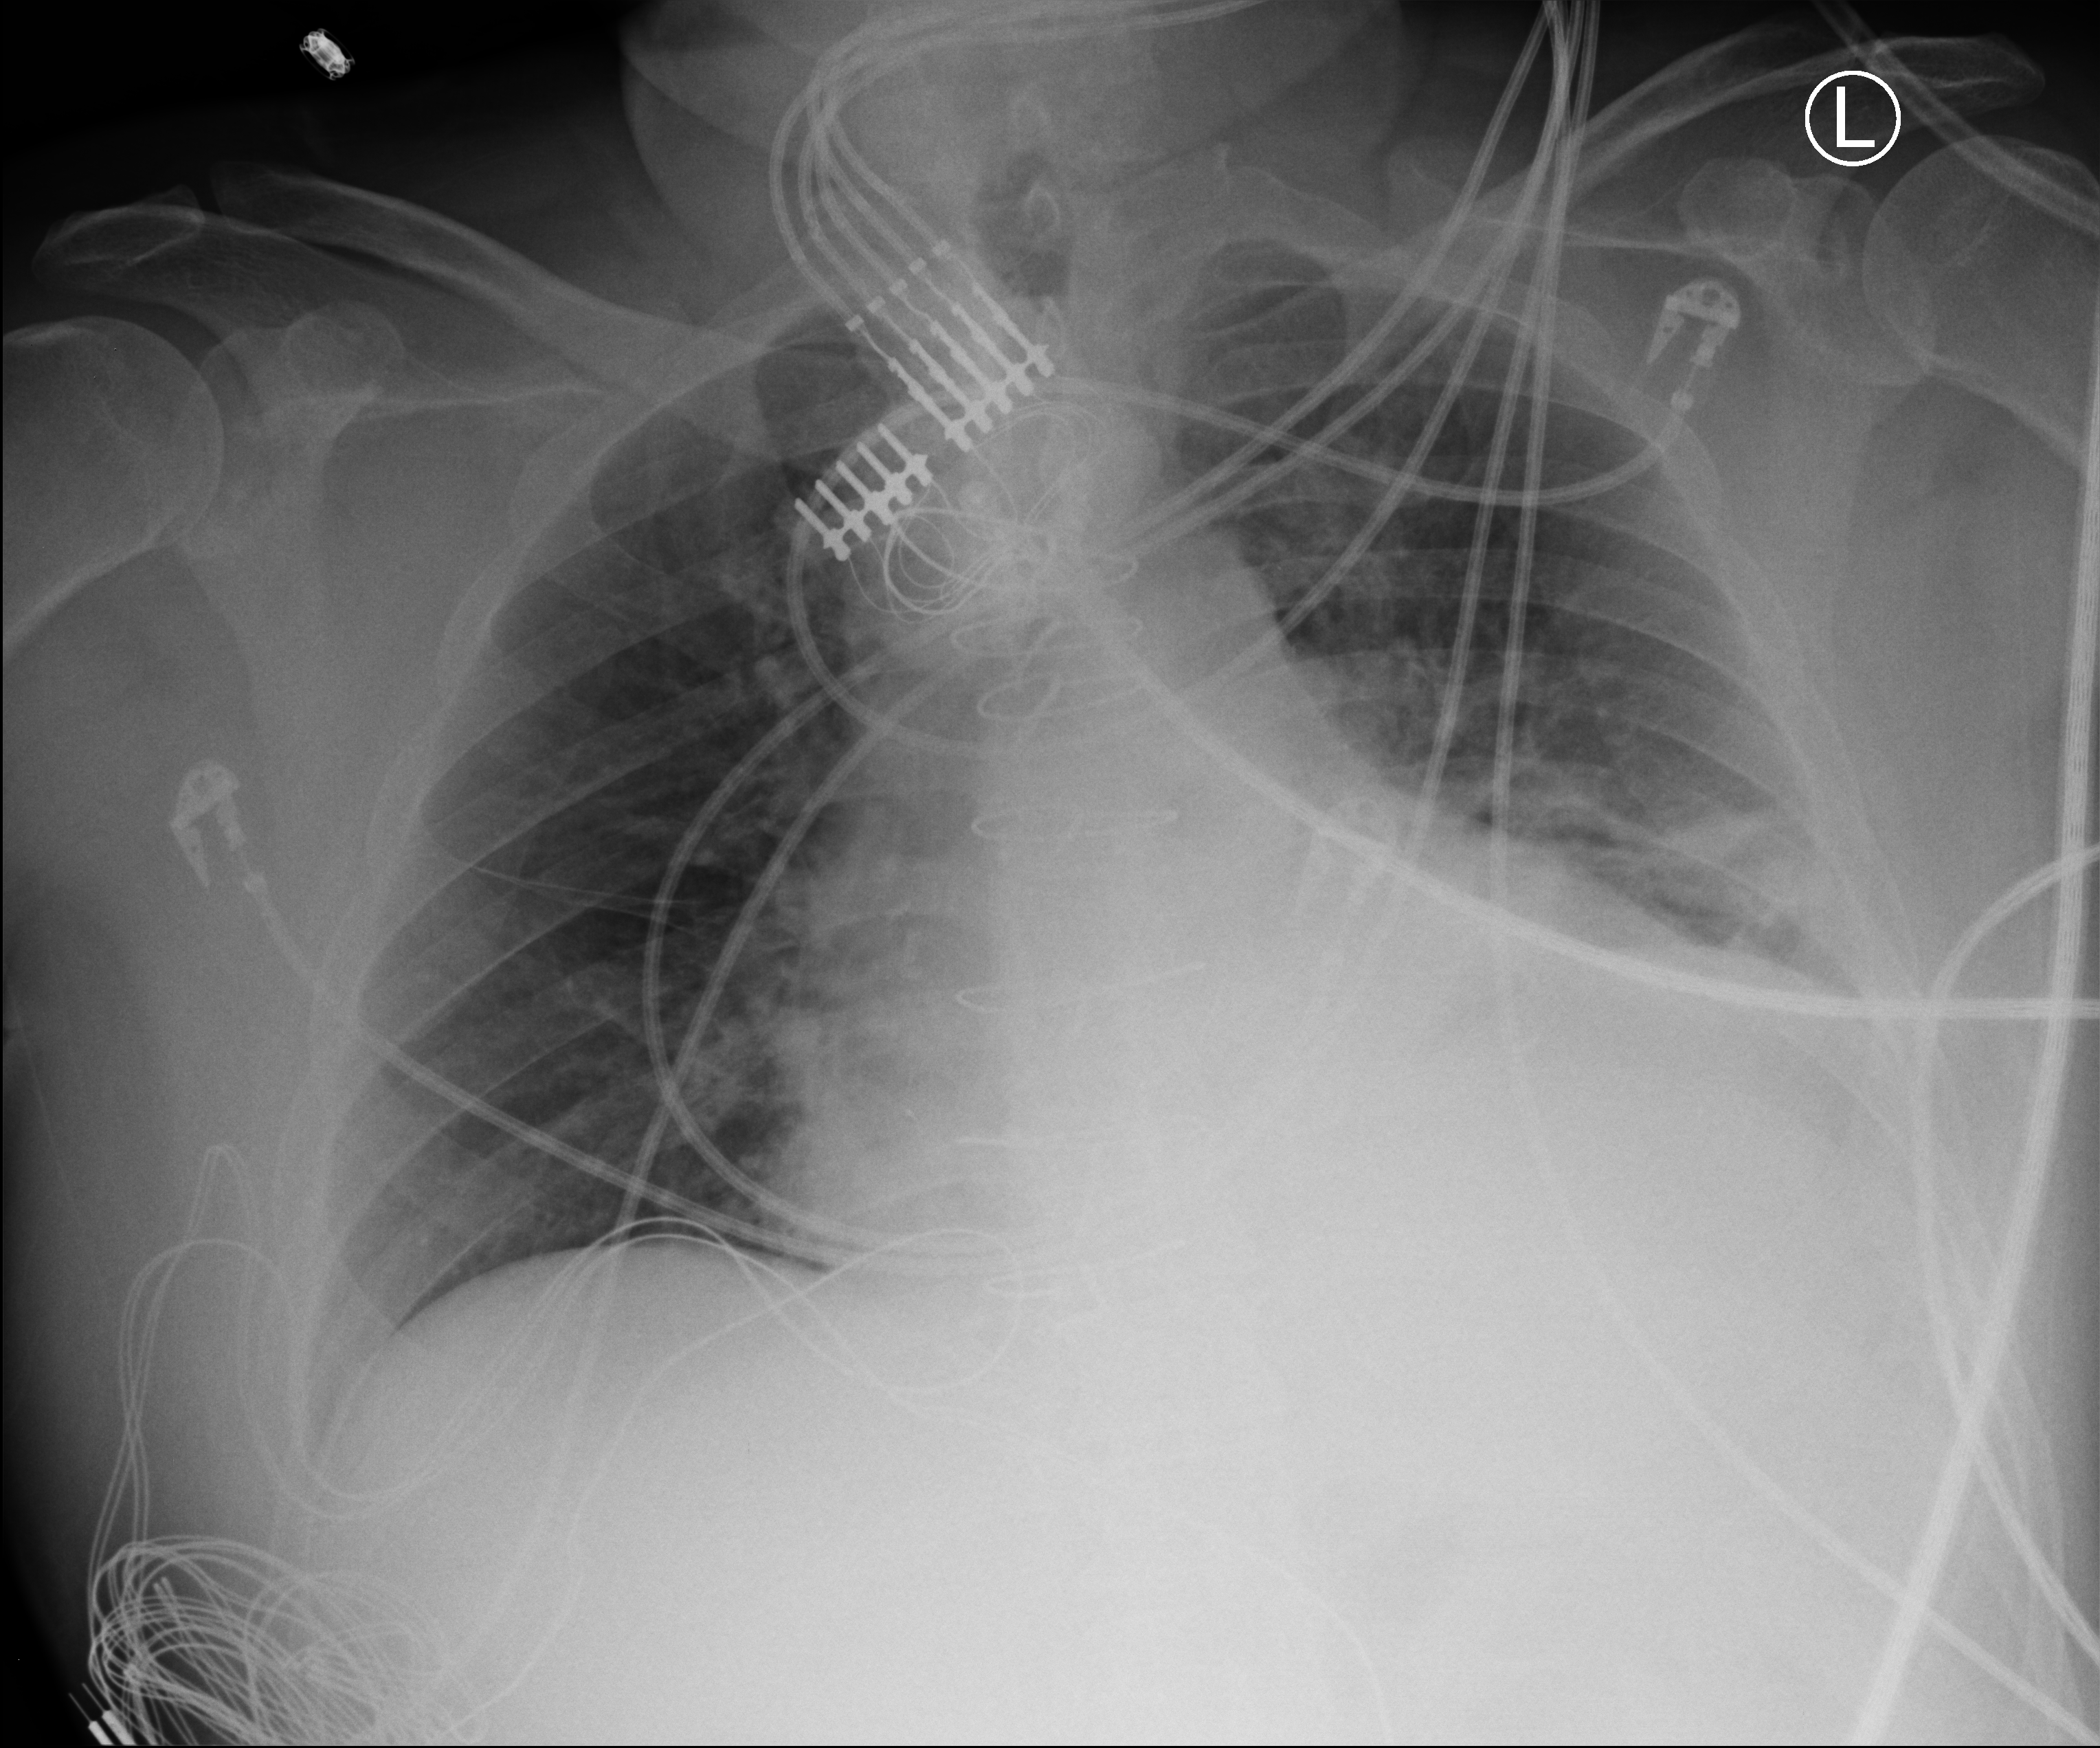
Portable chest radiograph, anteroposterior (AP) projection. Male patient hospitalised with COVID-19, age 18–59 years.
Admission-level facts for this patient (not findings on this image; timing relative to this image not recorded):
- mechanically ventilated during this hospital stay: no